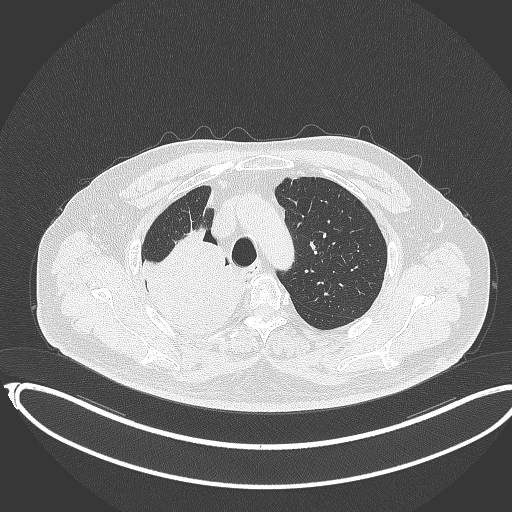
Chest CT, one axial slice. Position 286 of 403 along the scan axis. 120 kVp. Lung window (W 1500 / L -600 HU). 1 mm slice thickness. 512 × 512 image matrix, field of view 436 × 436 mm. Patient: male, 68 years. From the clinical record (not read from this slice): clinical TNM (as recorded): T2a N0 M0.
Structures marked on this image (bounding box drawn by a radiologist):
- lung tumour (recorded histology: adenocarcinoma): box from (x=135, y=229) to (x=260, y=343) px